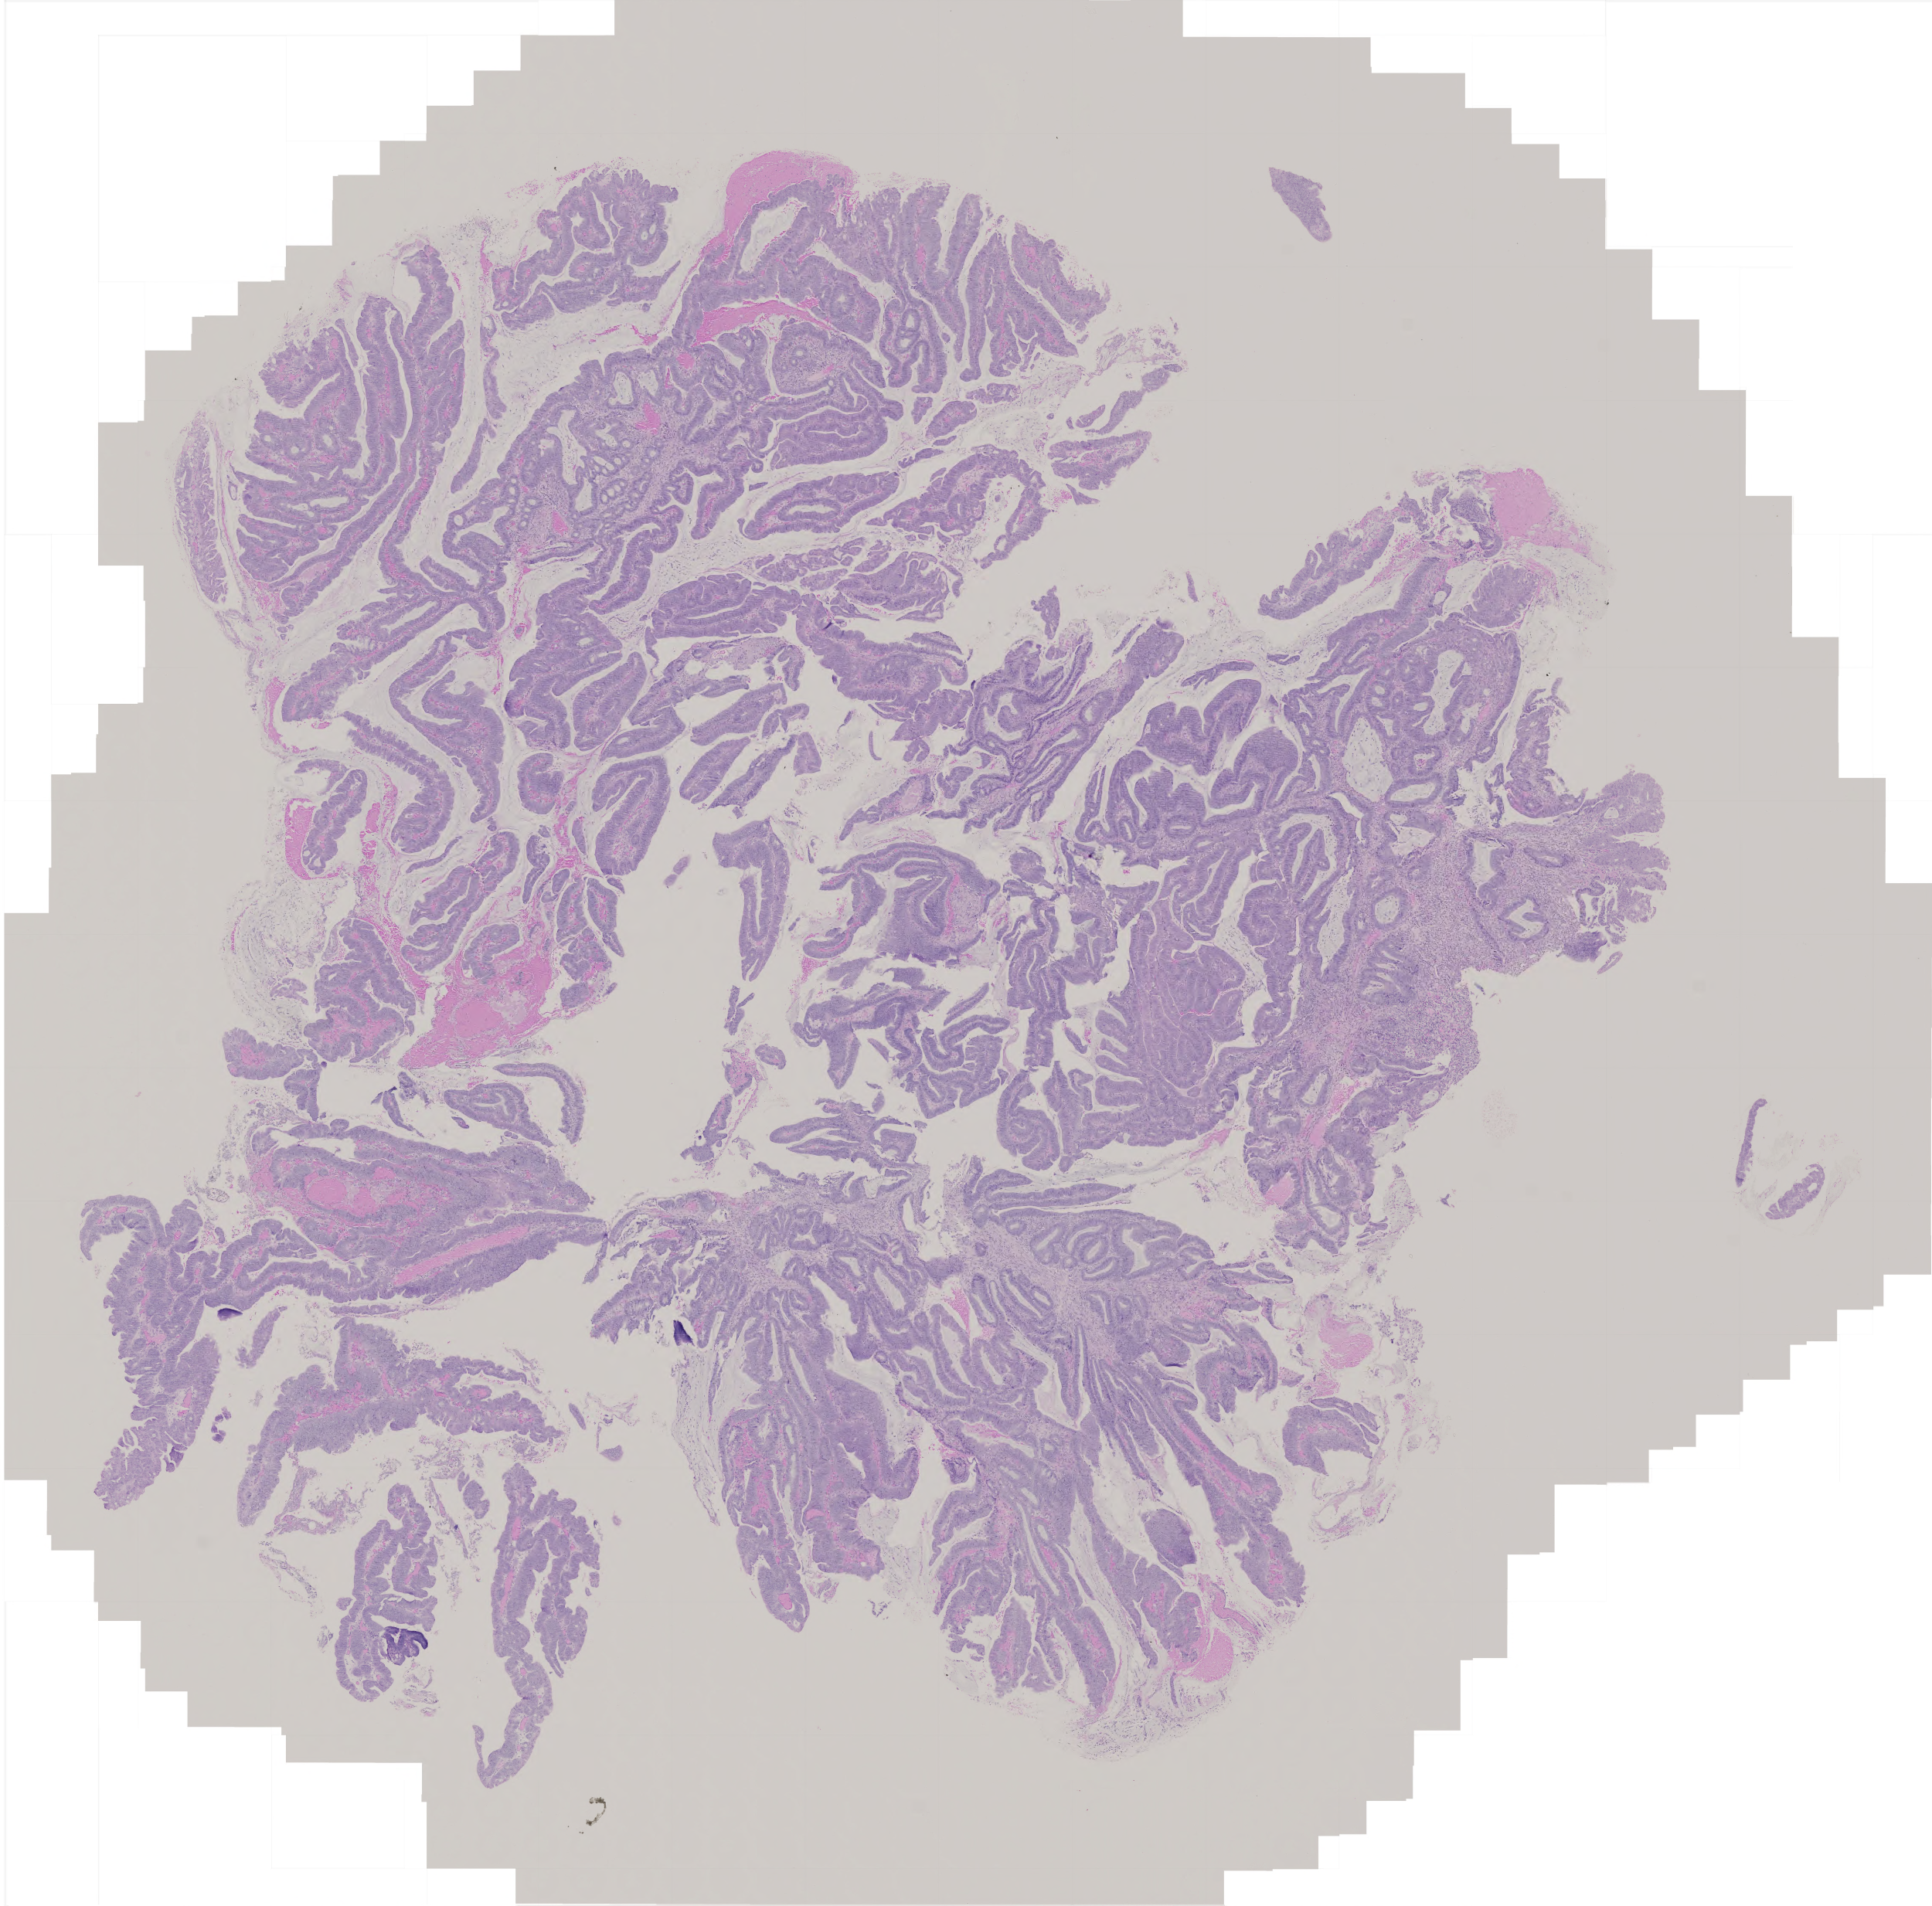
Hematoxylin and eosin (H&E) stained whole-slide image, whole scanned area (about 5.0 x 4.9 mm) shown as a low-resolution overview; formalin-fixed paraffin-embedded (FFPE) diagnostic section; primary tumour sample from the colon. Male patient; age at initial diagnosis 42 years.
Diagnosis: Adenocarcinoma, NOS (cecum). AJCC pathologic stage: II.